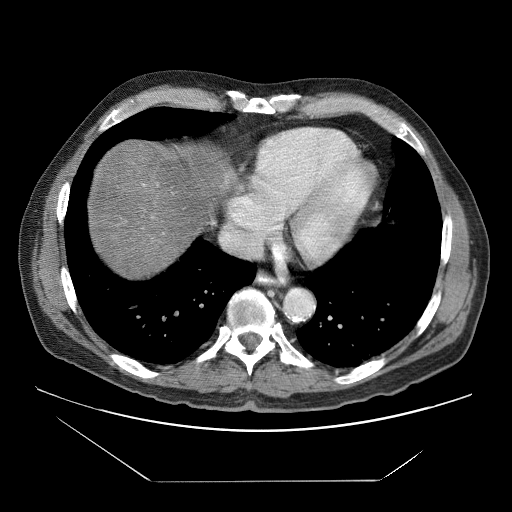
Contrast-enhanced abdominal CT (liver protocol), one axial slice. Position 70 of 83 along the scan axis. 120 kVp. Soft-tissue window (W 400 / L 40 HU). 2.5 mm slice thickness. 512 × 512 image matrix. From the clinical record (not read from this slice): diagnosis: hepatocellular carcinoma (patient treated with transarterial chemoembolisation; whether this scan precedes or follows treatment is not stated here); TNM stage (as recorded): Stage-IVB; Child-Pugh class: B; tumour nodularity: uninodular.
Annotated regions visible in this slice (semi-automatic segmentation, software-assisted and operator-edited):
- liver parenchyma outside the tumour (the mass and vessels are separate outlines, so this box may not span the whole liver): bounding box <88,140,228,276> (left, top, right, bottom; pixels)
- liver vessels: <143,184,146,187>